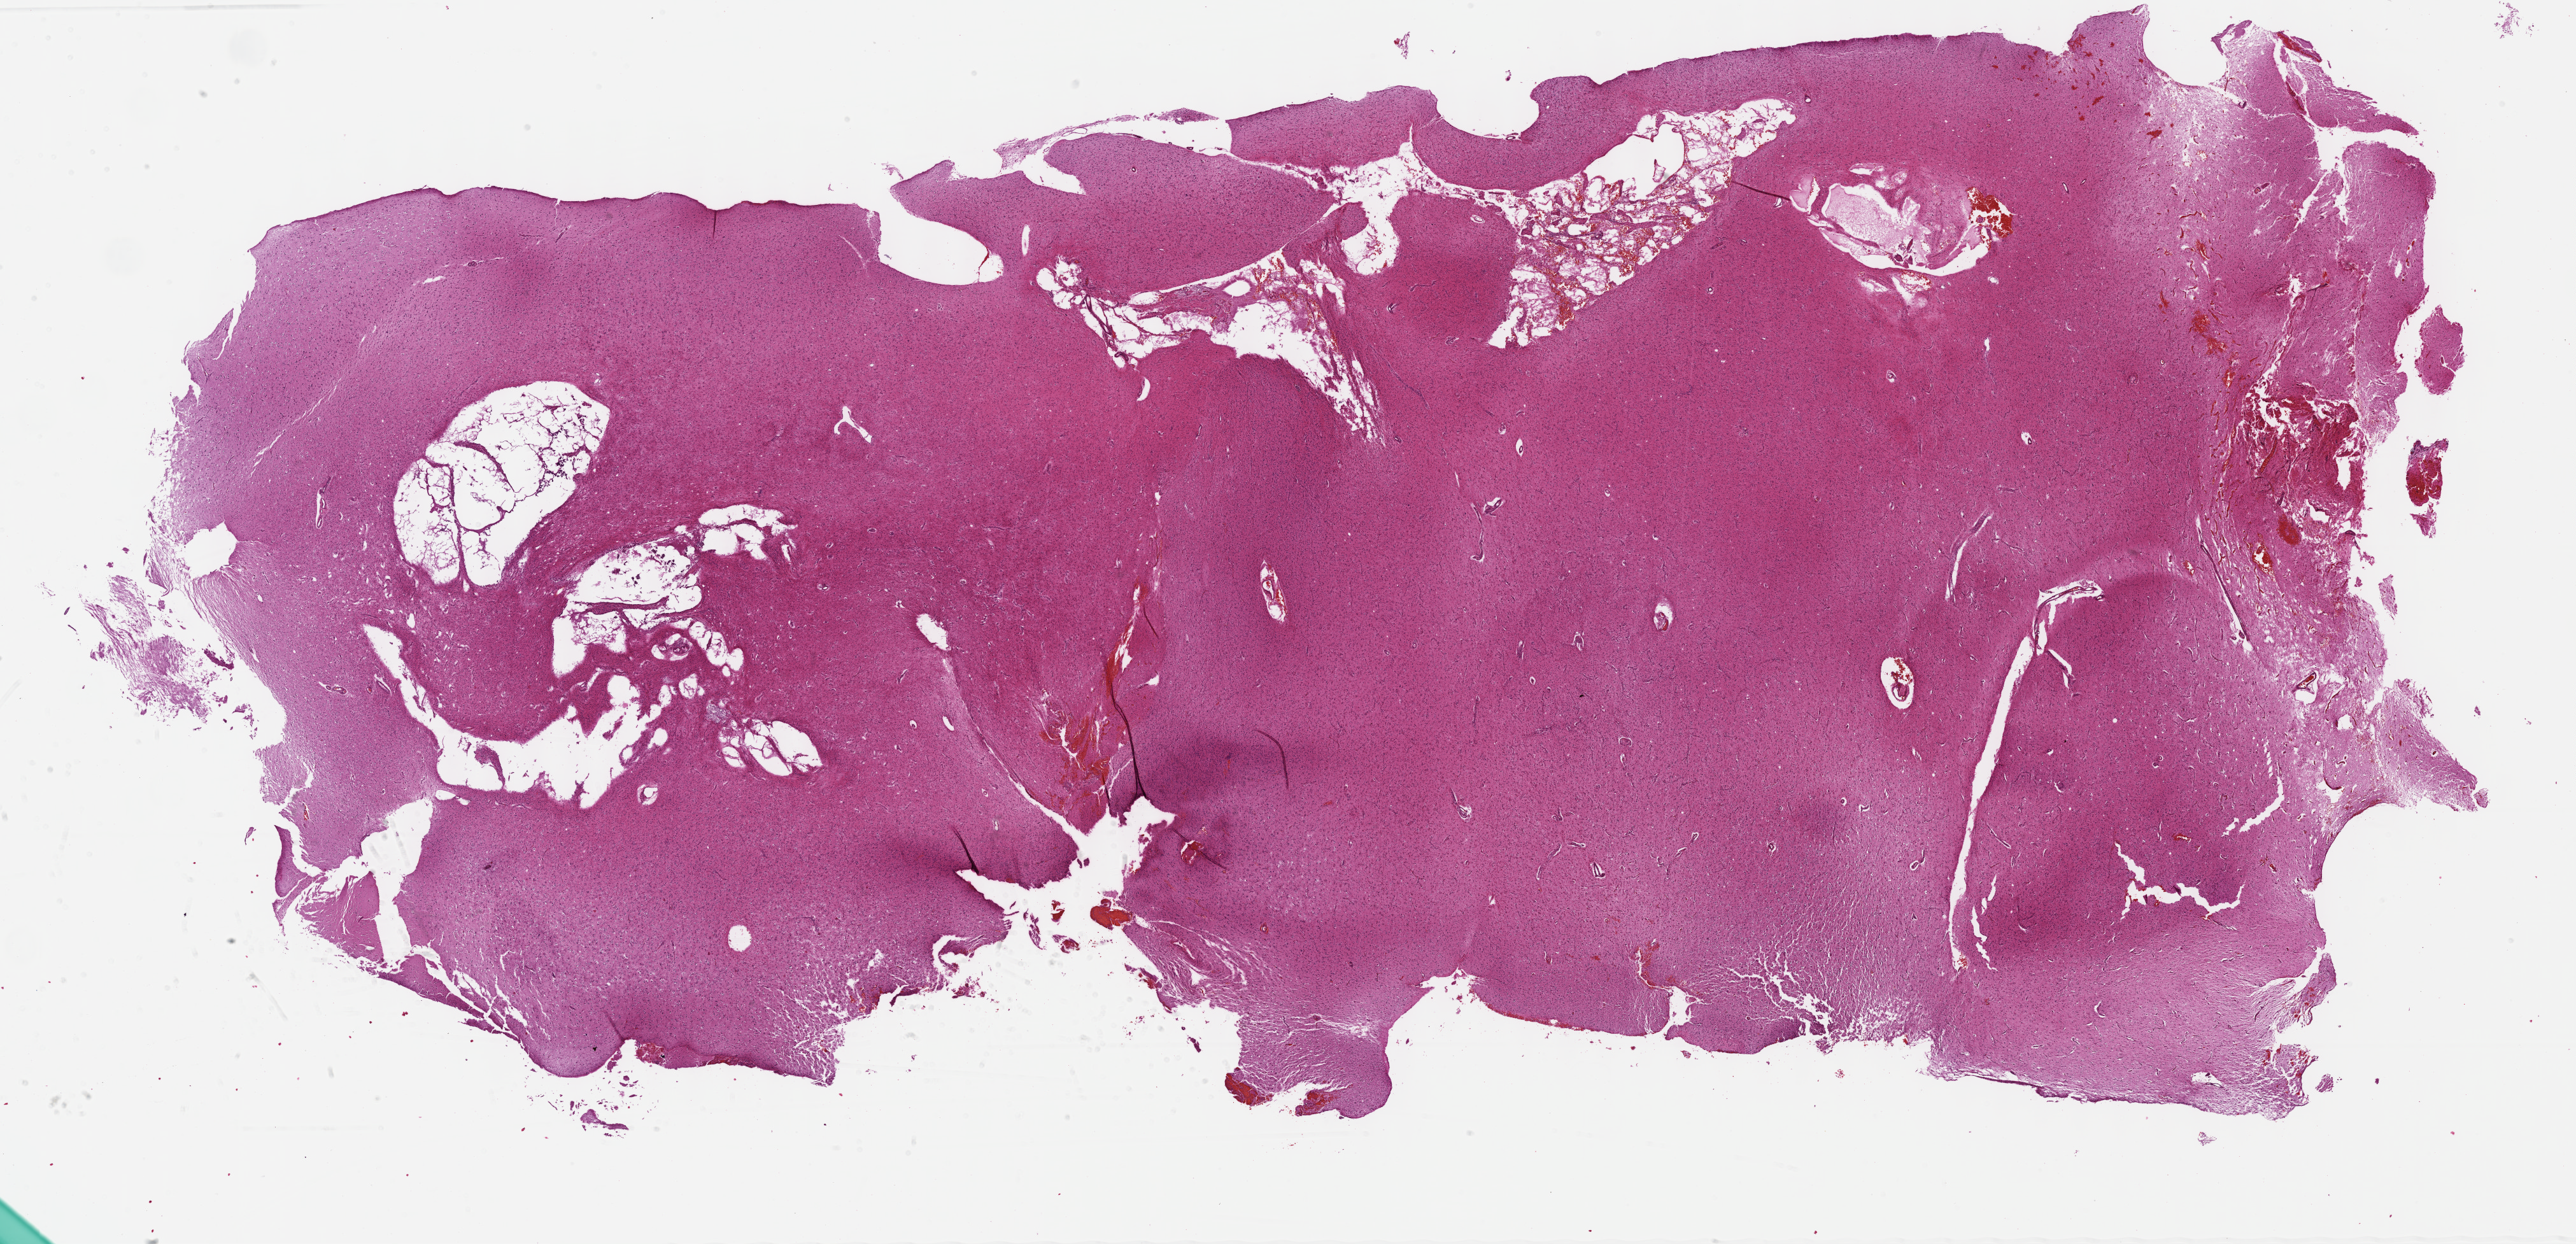
Hematoxylin and eosin (H&E) stained whole-slide image — shown as a low-resolution overview of the whole scanned area (about 32.7 x 15.8 mm, slide scanned at 40x); formalin-fixed paraffin-embedded (FFPE) diagnostic section; brain, primary tumour sample. Female, age 32 years at initial diagnosis. Histologic grade: G3 (poorly differentiated).
* pathologic diagnosis: Astrocytoma, anaplastic (cerebrum)